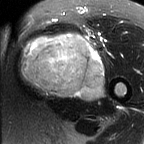
MRI of an extremity soft-tissue mass, one axial slice; position 39 of 60 along the scan axis; T2-weighted fat-saturated; MR volume resampled by the dataset authors to the PET/CT grid (not the native acquisition matrix); 3.27 mm slice thickness; 144 × 144 image matrix. Female patient. Case-level facts recorded for this patient, not image findings: histological type: pleiomorphic leiomyosarcoma; grade: intermediate; site of the primary tumour: left thigh.
Structures marked on this image (expert contour drawn on MRI and transferred to this co-registered scan by the dataset authors):
- gross tumour volume including surrounding oedema: bounding box <18,31,105,100> (left, top, right, bottom; pixels)
- gross tumour volume (mass): <18,33,105,100>